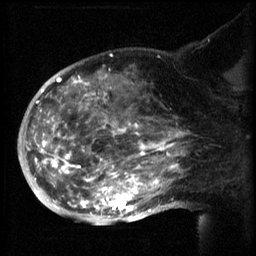
Breast MRI (dynamic contrast-enhanced), one sagittal slice; slice 38 of 60 in the series (ordered by position); 3 images stored at this slice position (order not interpretable as contrast timing); 1.5 T; TE 4.2 ms, TR 8.2 ms; 256 × 256 image matrix. Patient: female, 50 years.
Structures marked on this image (semi-automatically segmented with operator editing):
- analysis volume of interest (the breast-tissue region the enhancement analysis was run in; not a lesion): bounding box <50,64,169,217> (left, top, right, bottom; pixels)
- tumour enhancement mask (voxels above the 70 % enhancement threshold inside the analysis volume of interest): <50,66,169,215>